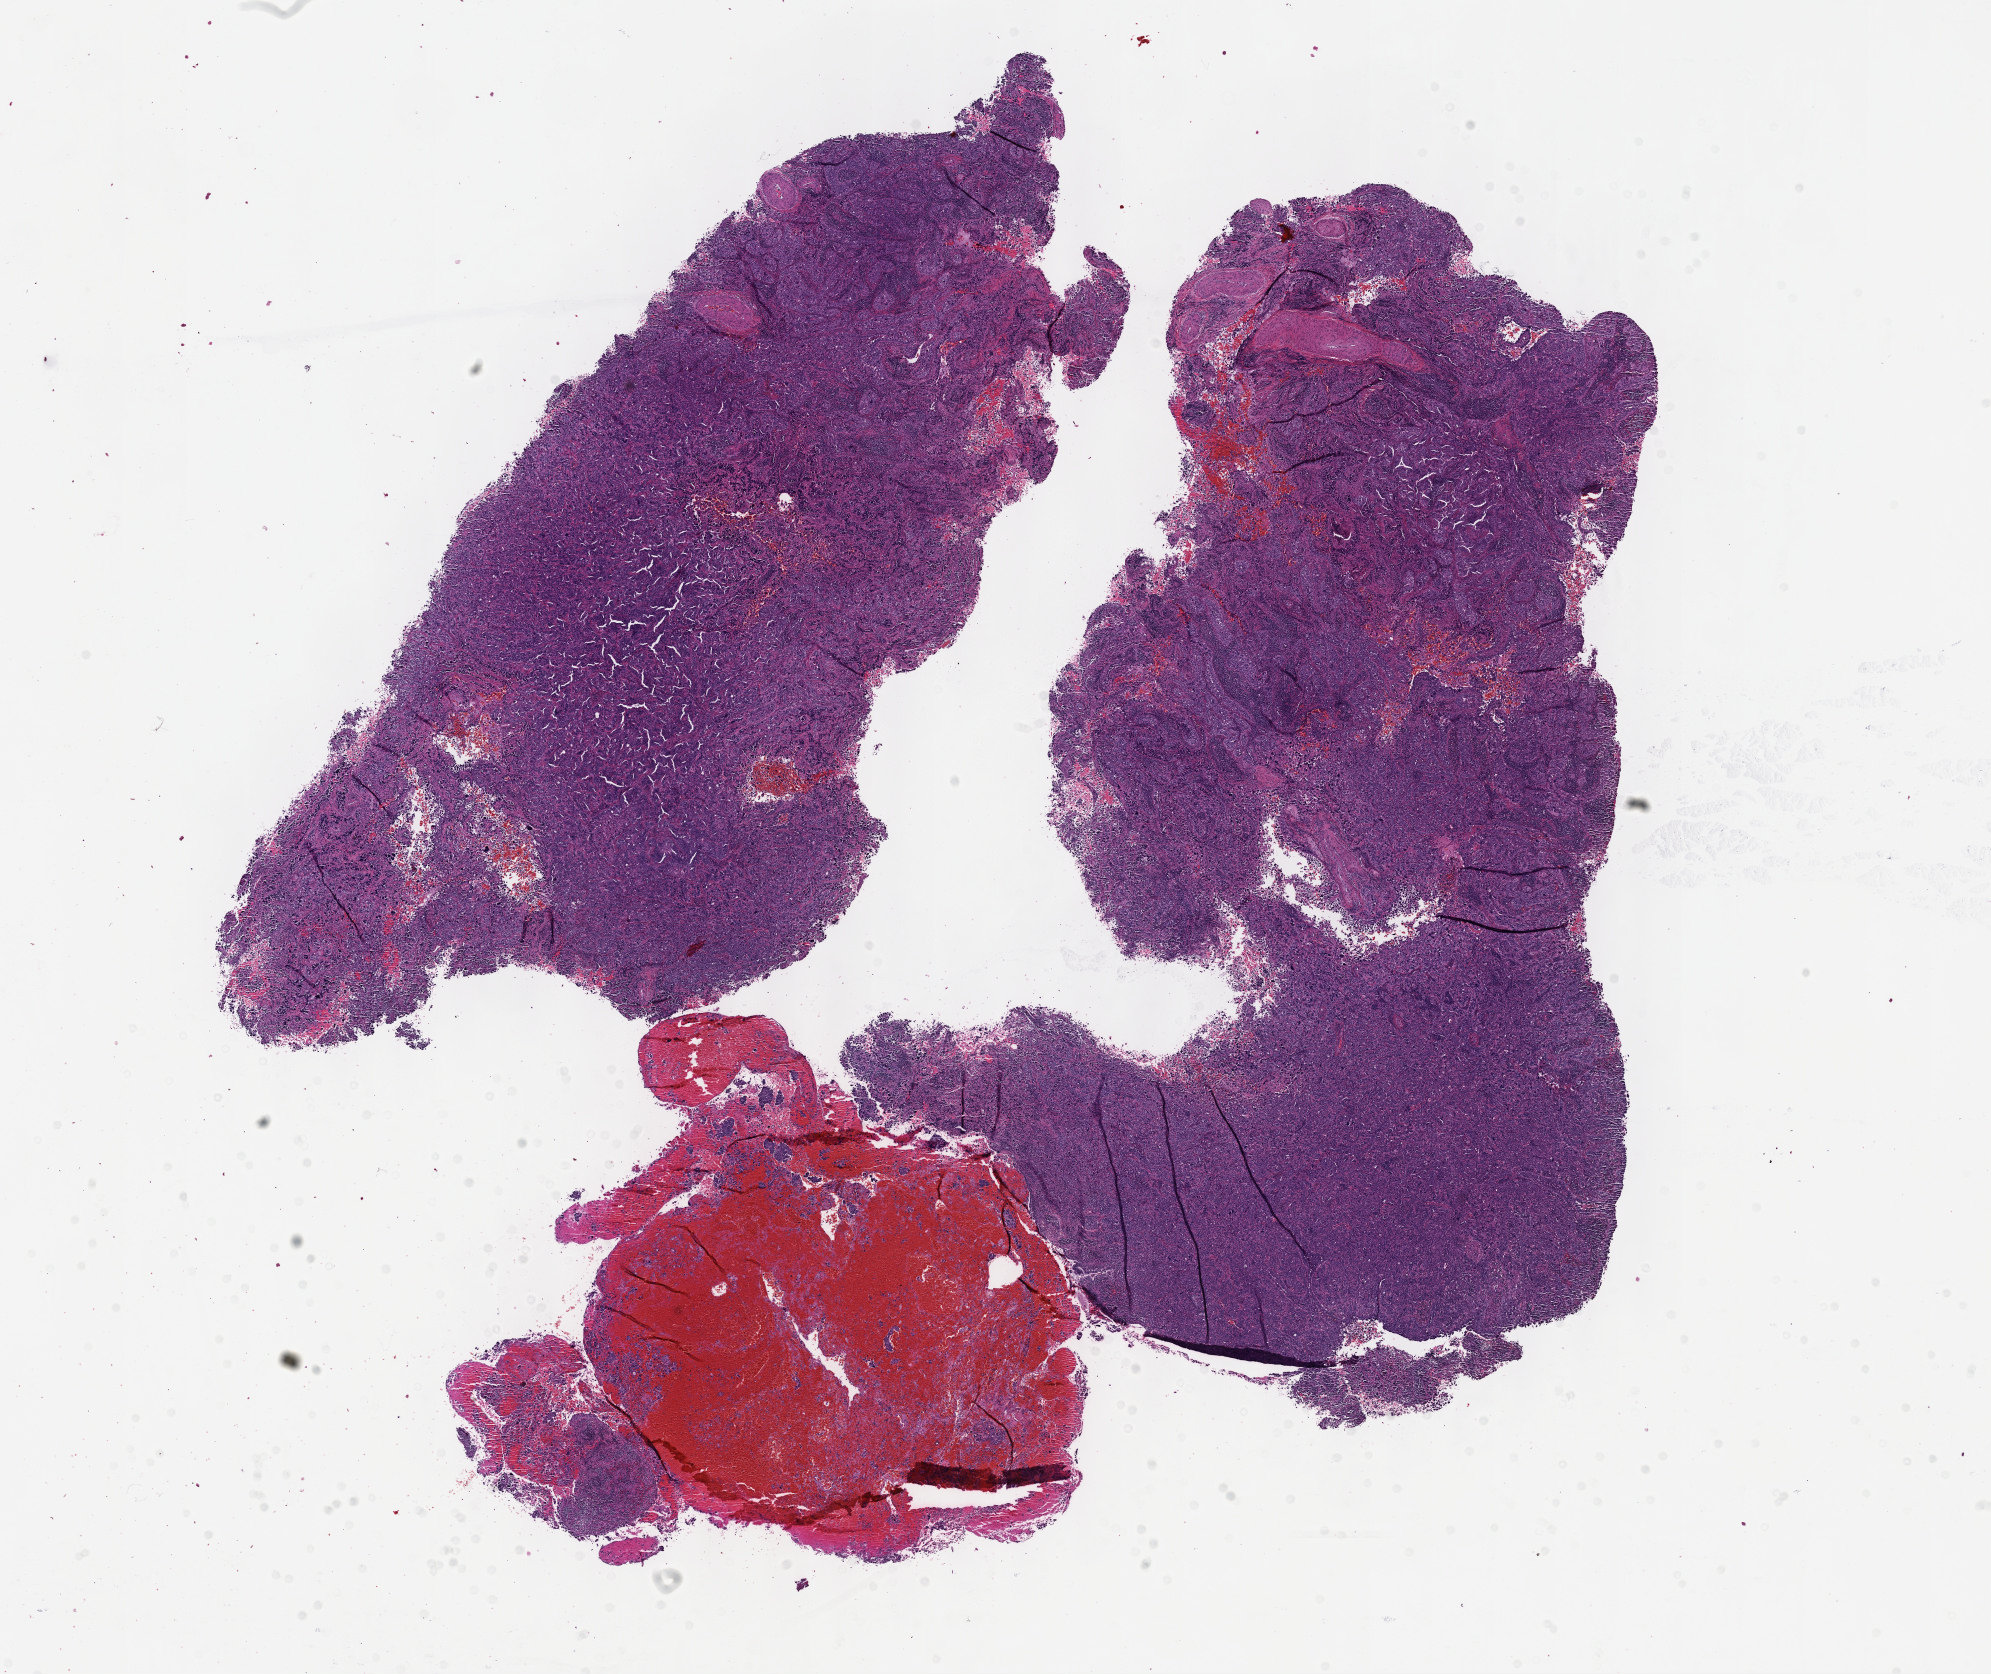
Hematoxylin and eosin (H&E) stained whole-slide image, shown as a low-resolution overview of the whole scanned area (about 16.1 x 13.5 mm), formalin-fixed paraffin-embedded (FFPE) diagnostic section, primary tumour sample from the cervix. Patient: female, age at initial diagnosis 34 years. Histologic grade: GX (grade cannot be assessed).
FIGO stage: IIB. Lymph nodes positive (case pathology): 0 of 4 examined. Histologic diagnosis: Squamous cell carcinoma, NOS (cervix uteri).